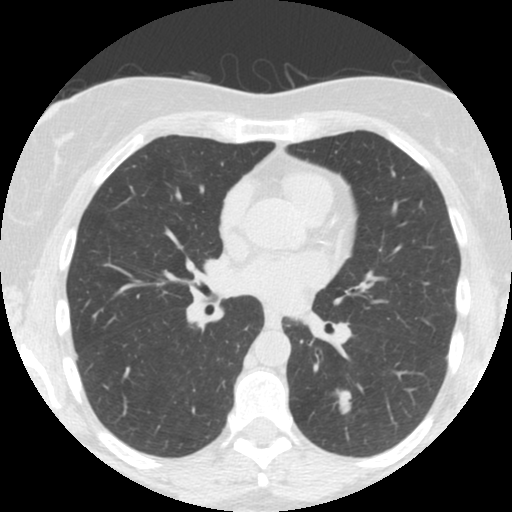
Low-dose screening chest CT, one axial slice. Slice 80 of 150 in the series (ordered by position). 120 kVp. Lung window (W 1500 / L -600 HU). 2.5 mm slice thickness. 512 × 512 image matrix.
Annotated regions visible in this slice (expert manual segmentation):
- lesion 1 (tumor, lower lobe of left lung): box from (x=339, y=390) to (x=352, y=414) px